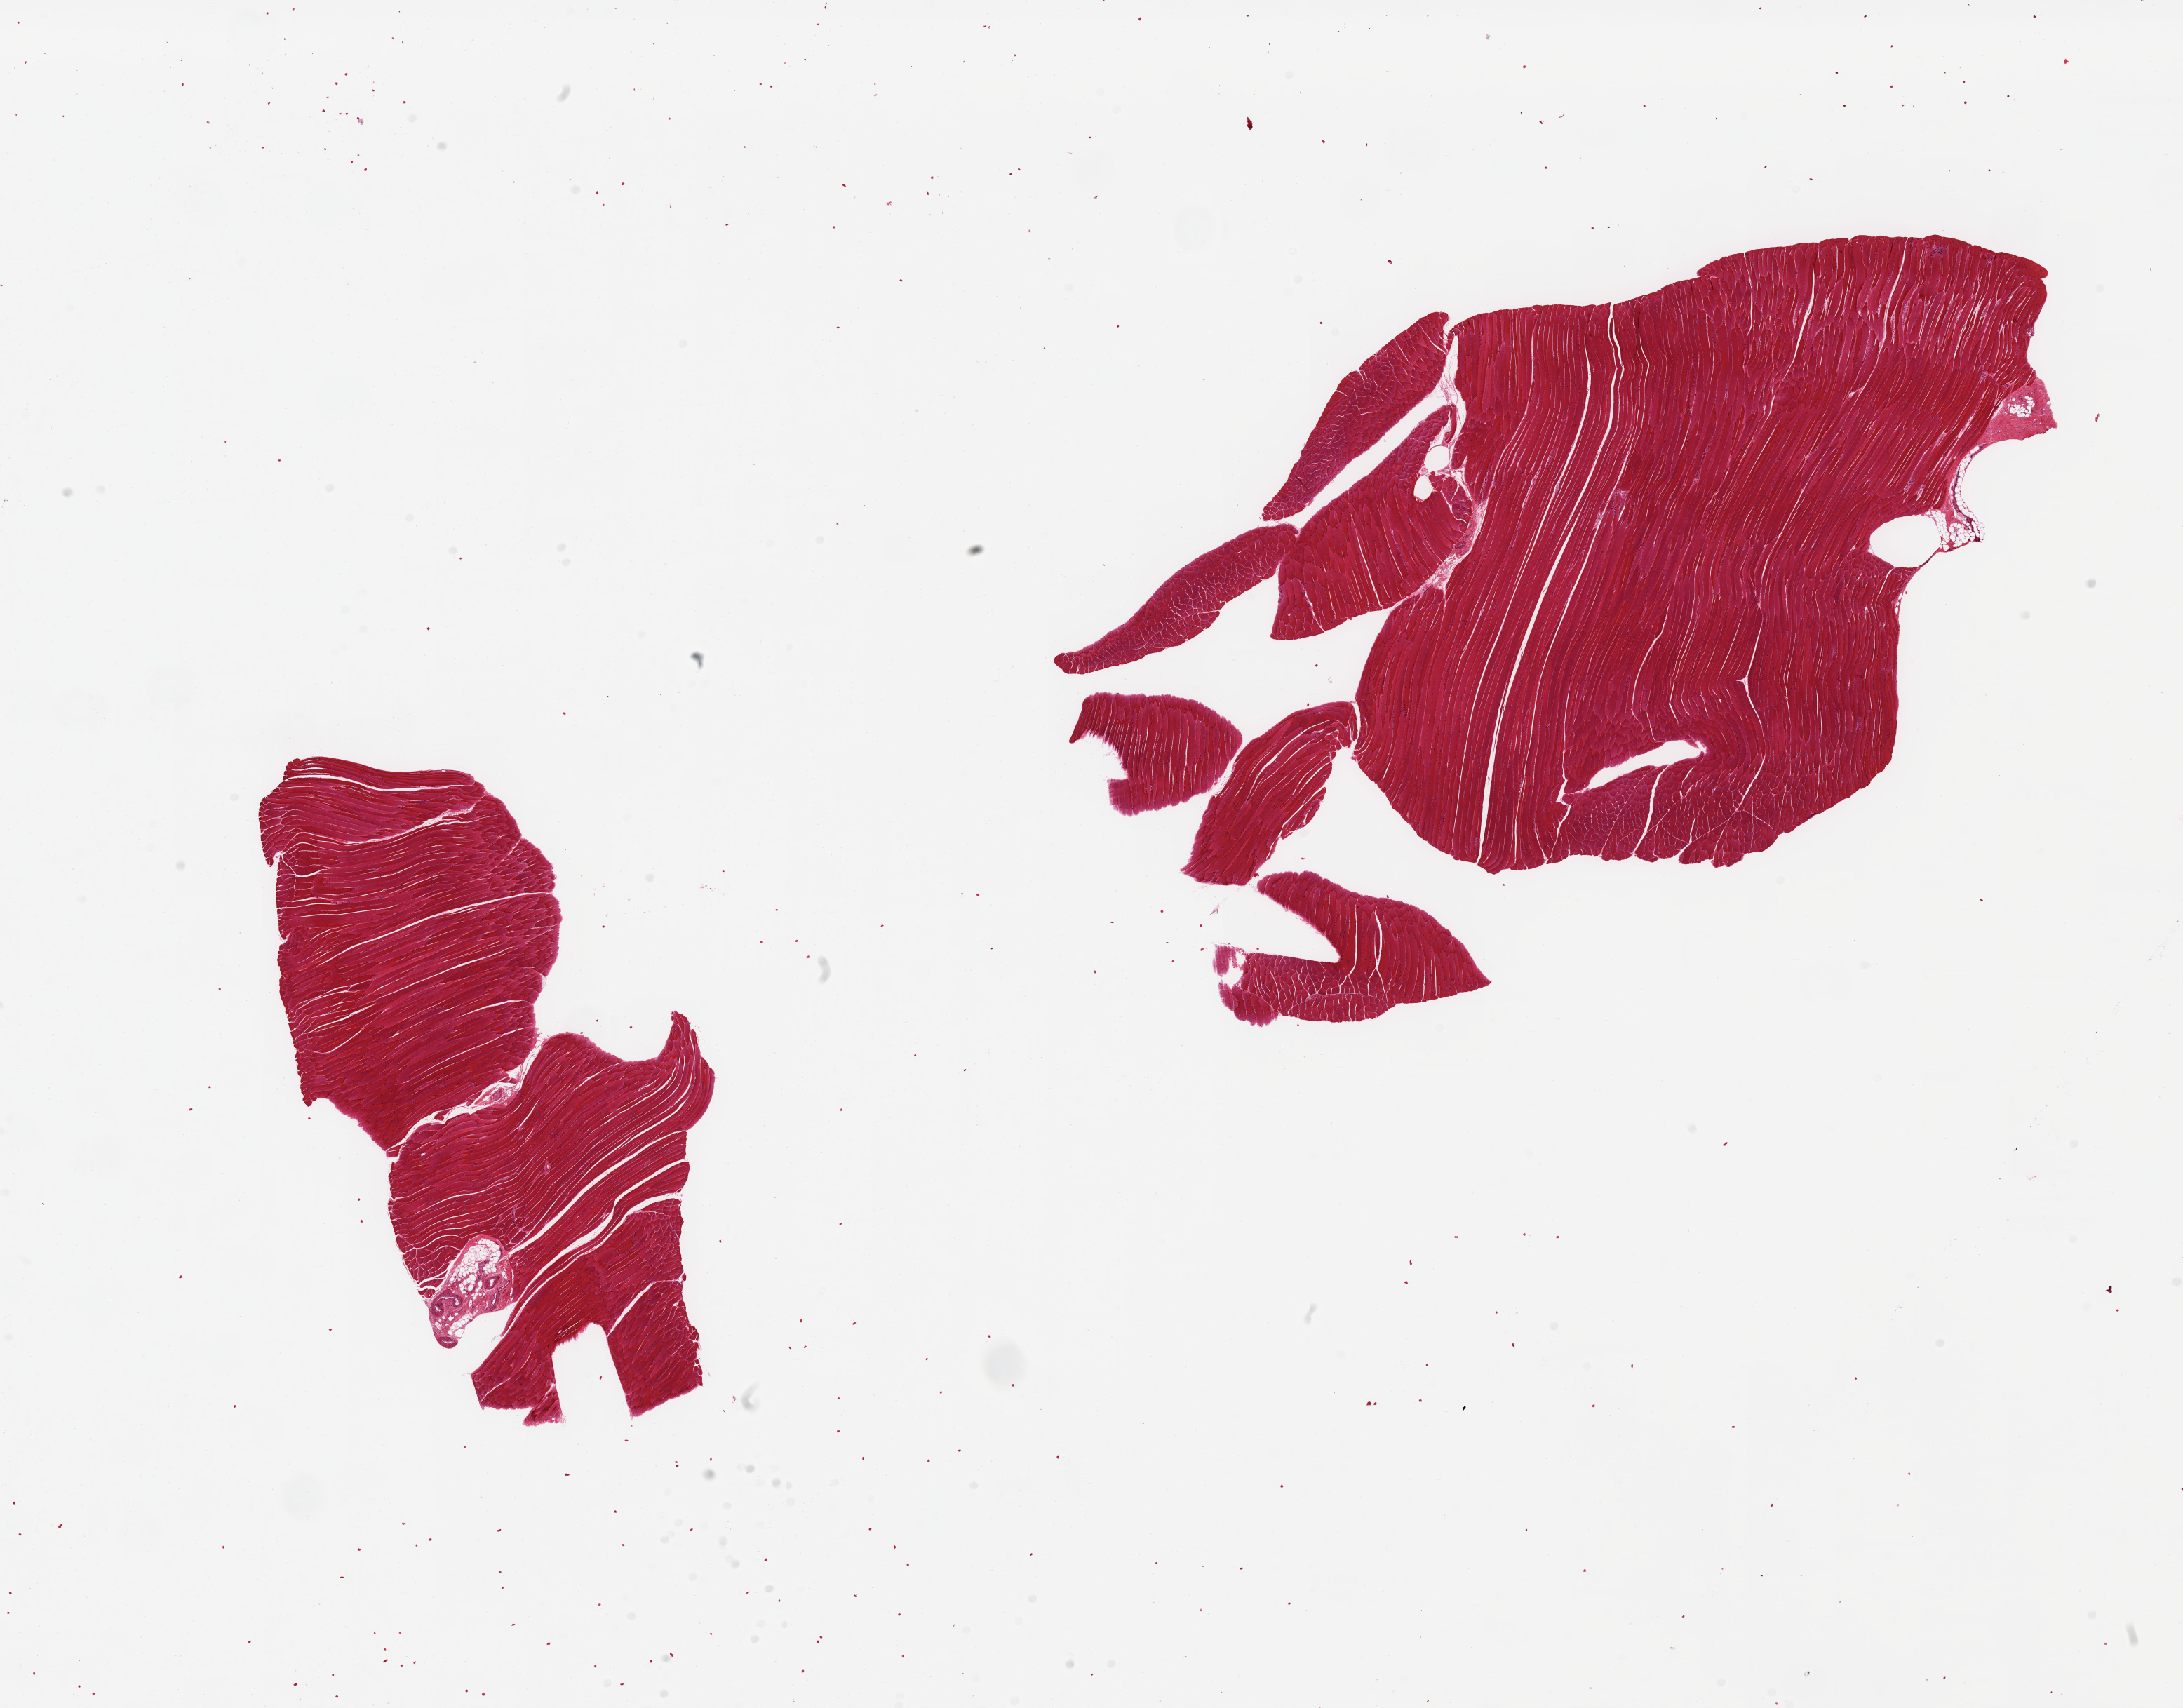
H&E whole-slide image — shown as a low-resolution overview of the whole scanned area (about 24.6 x 19.3 mm, acquisition: 20x scan); PAXgene-fixed paraffin-embedded (PFPE) section; target tissue: skeletal muscle; donor tissue sample. Donor: male.
Reviewer comment on this tissue sample: 2 pieces; interstitial lymphocytes (myositis?); small foci of fibrovascular and adipose tissue.